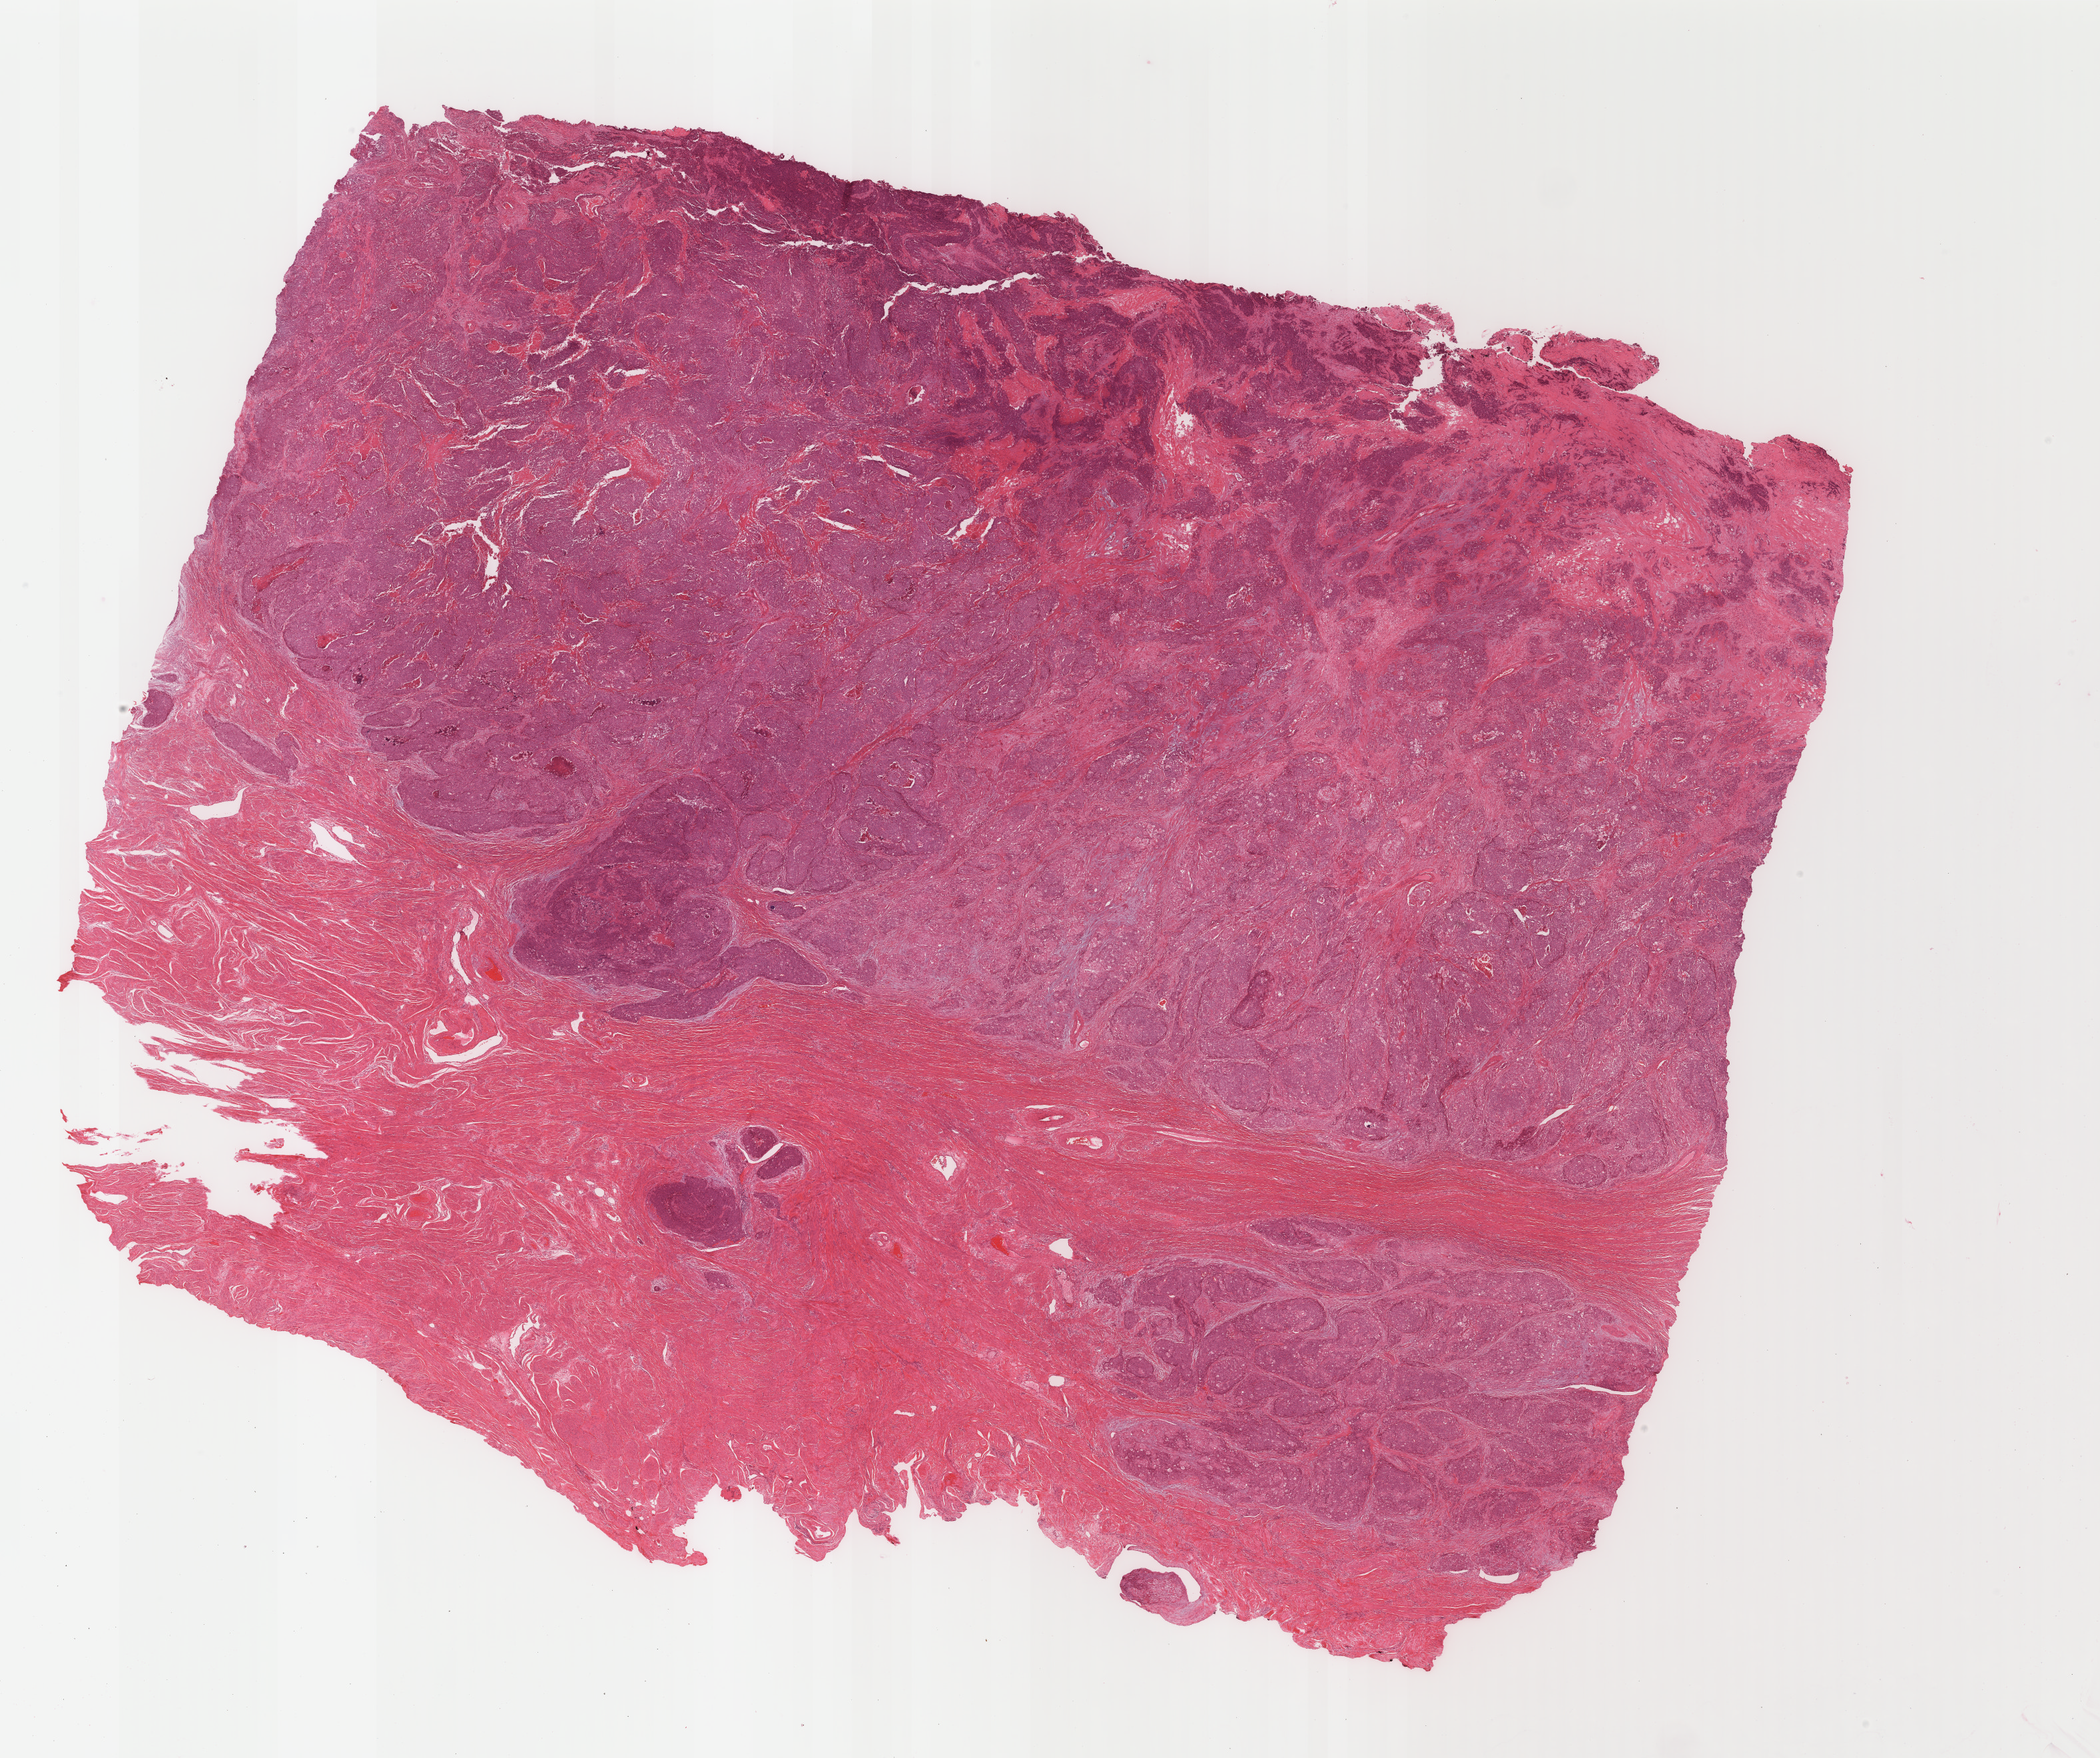
Digitized H&E tissue section (whole slide) — whole scanned area (about 25.0 x 21.0 mm, slide scanned at 40x) shown as a low-resolution overview. Formalin-fixed paraffin-embedded (FFPE) diagnostic section. Uterus, primary tumour sample. Female, age 54 years at initial diagnosis. Histologic grade: G3 (poorly differentiated).
FIGO stage: IIB. Histologic diagnosis: Endometrioid adenocarcinoma, NOS (endometrium).